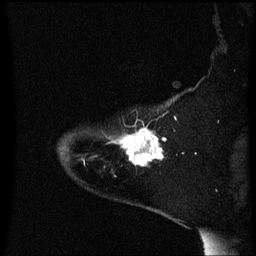
Breast MRI (dynamic contrast-enhanced), one sagittal slice. Slice 50 of 60 in the series (ordered by position). Dynamic contrast-enhanced series, image 2 of 3 at this slice position (ordered by acquisition). 1.5 T. TE 4.2 ms, TR 8.4 ms. 2 mm slice thickness. 256 × 256 image matrix, field of view 200 × 200 mm. Female patient, age 54 years. From the clinical record (not read from this slice): setting: breast cancer imaged before/during neoadjuvant chemotherapy; receptor status: HR-positive, HER2-negative.
Outlined on this slice (semi-automatic segmentation, software-assisted and operator-edited):
- analysis volume of interest (the breast-tissue region the enhancement analysis was run in; not a lesion): bounding box [x1, y1, x2, y2] px = [117, 128, 167, 167]
- tumour enhancement mask (voxels above the 70 % enhancement threshold inside the analysis volume of interest): [122, 128, 167, 167]